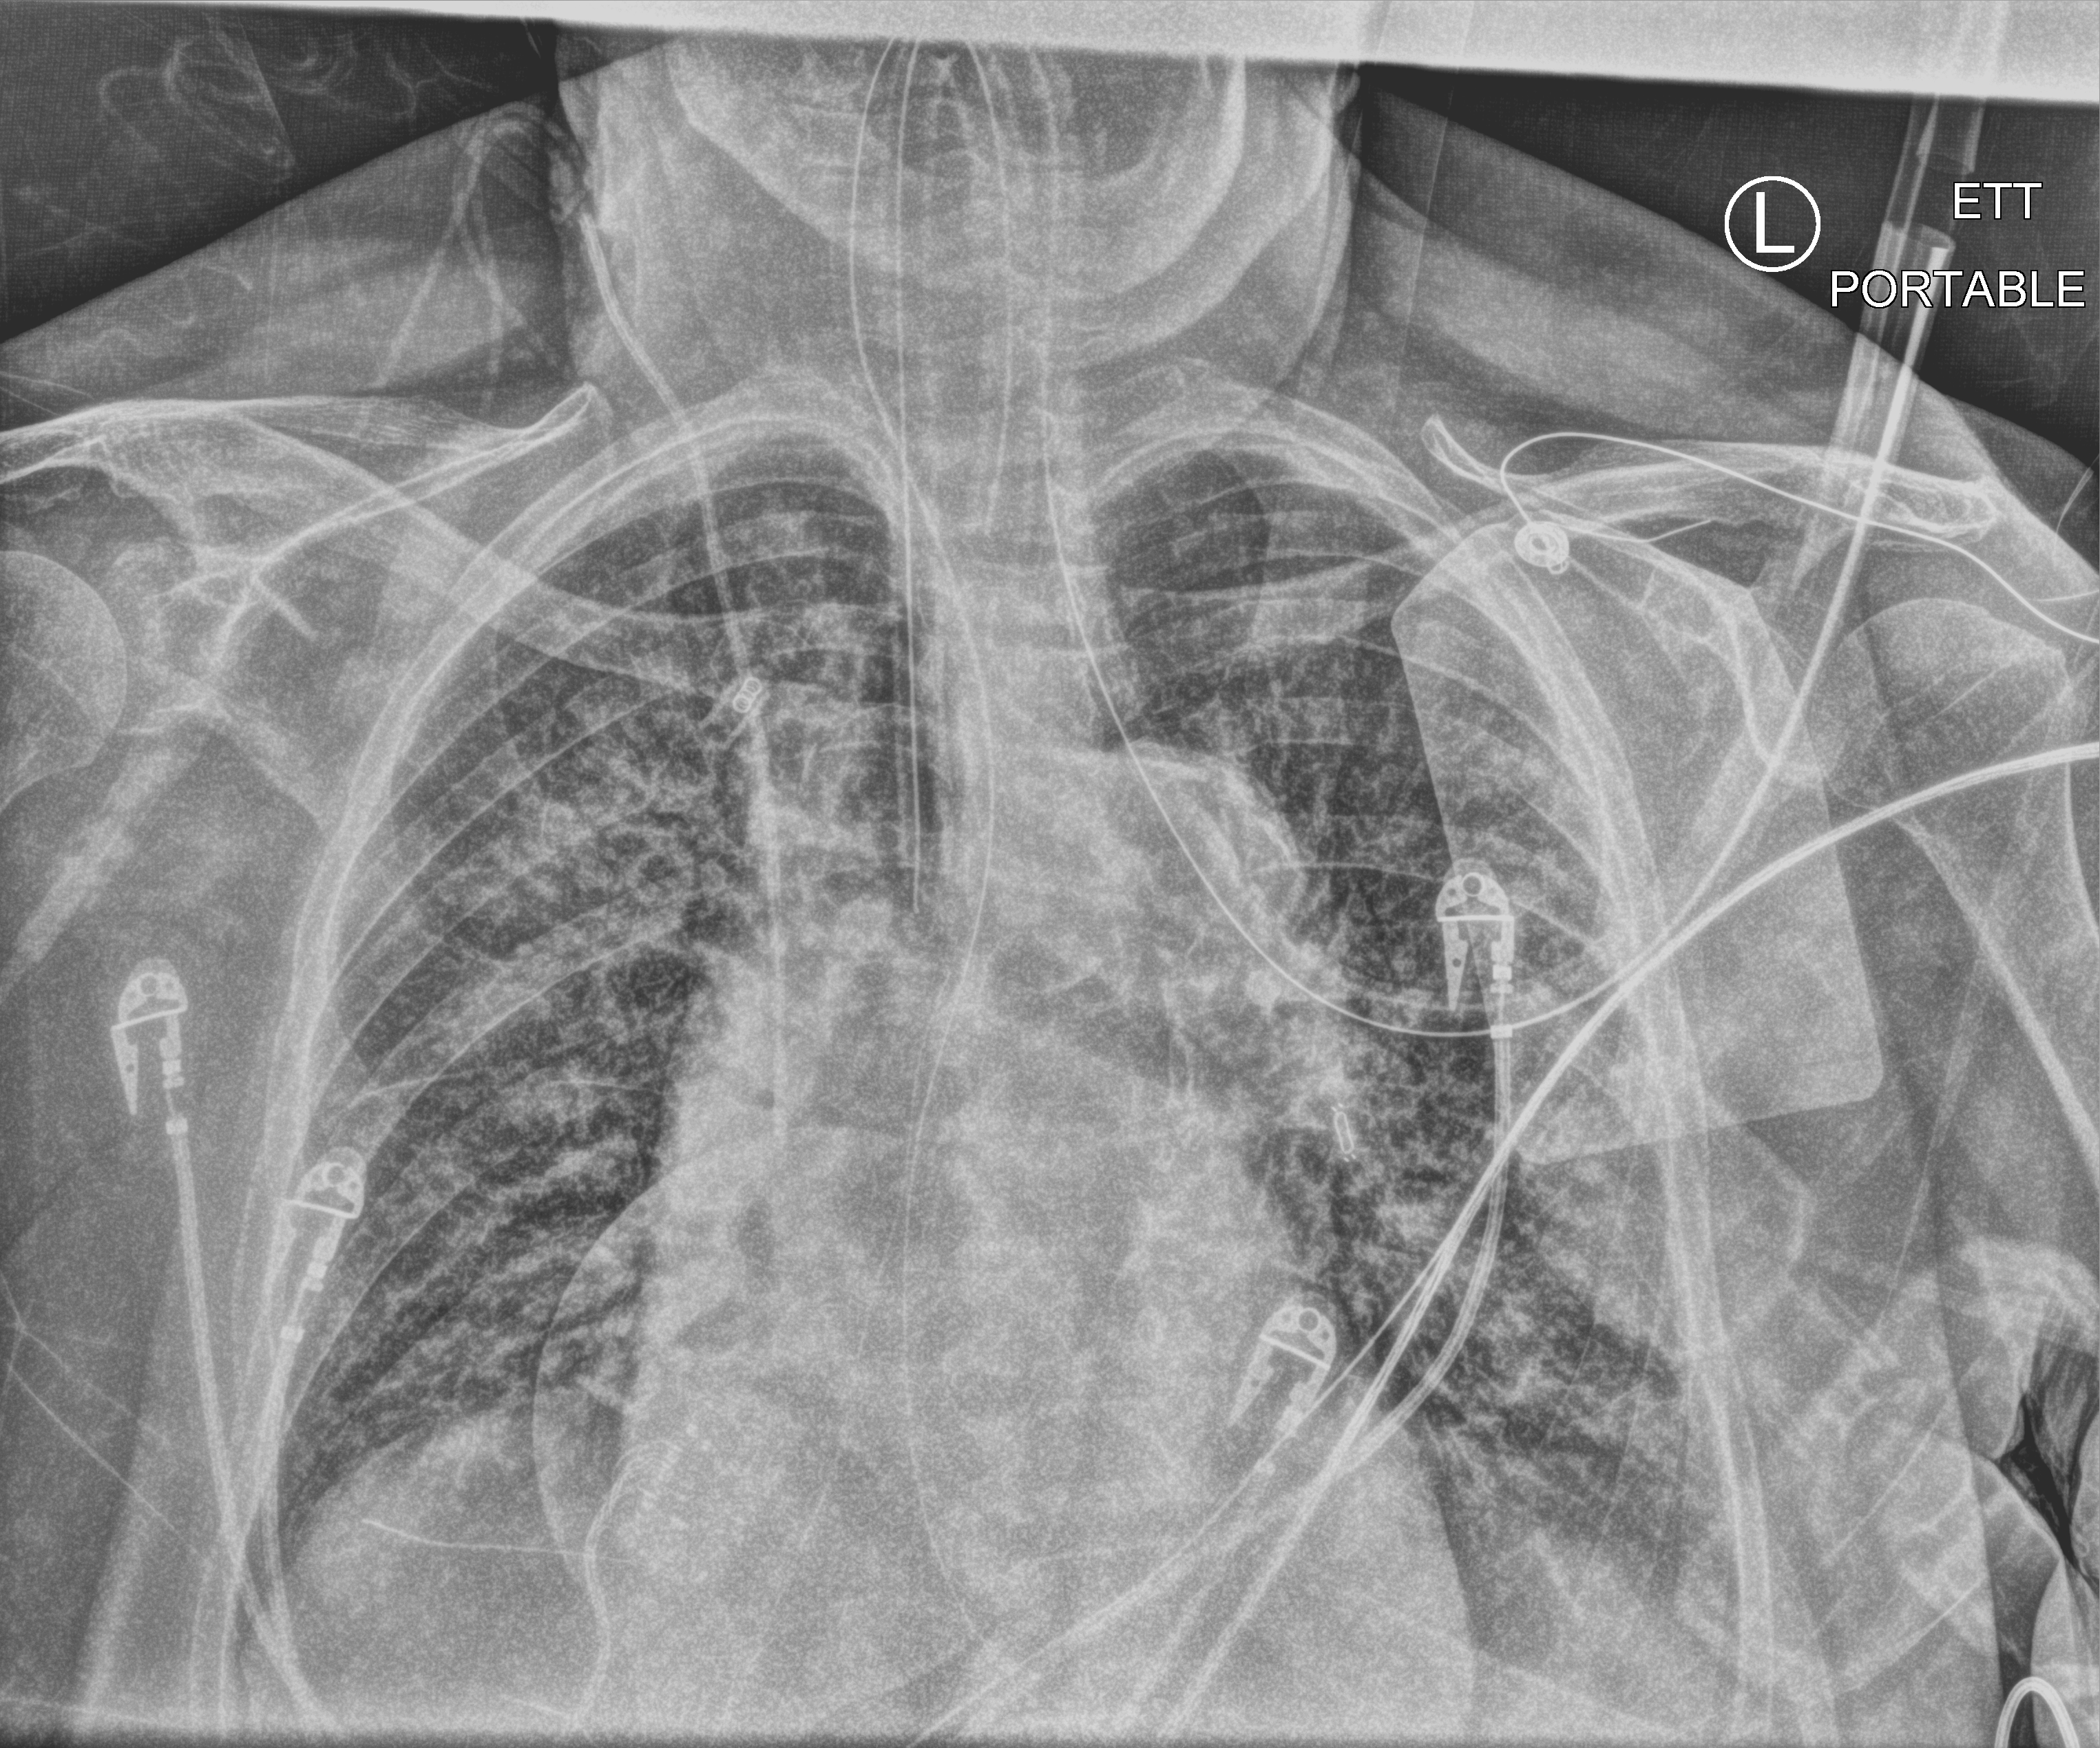
Bedside chest radiograph (computed radiography), anteroposterior (AP) projection. Patient hospitalised with COVID-19; female, aged 75–90 years.
Hospital-stay facts (about this admission, not read from this image; timing relative to this image not recorded): mechanically ventilated during this hospital stay: yes; hypertension (admission record): yes.